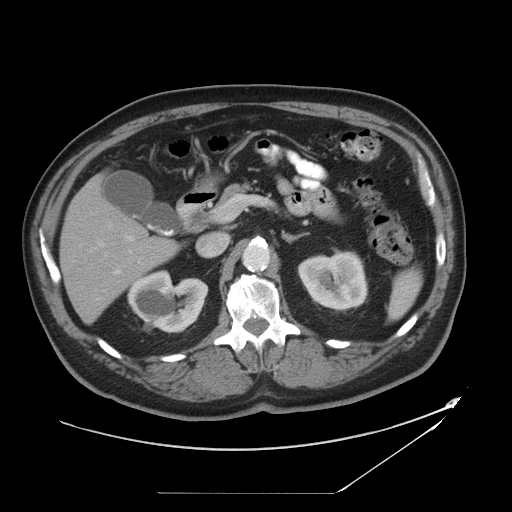
Contrast-enhanced abdominal CT, one axial slice. Slice 23 of 49 in the series (ordered by position). Soft-tissue window (W 400 / L 40 HU). 5 mm slice thickness. 512 × 512 image matrix. Male patient, age 72 years. From the clinical record (not read from this slice): diagnosis: colorectal cancer liver metastases, imaged before liver resection; multiple liver metastases: no; largest metastasis: 2.5 cm; disease in both lobes: no.
Structures marked on this image (manually delineated by an expert):
- hepatic veins: bounding box <97,223,112,247> (left, top, right, bottom; pixels)
- liver: <62,182,176,321>
- planned liver remnant (the part of the liver to remain after resection): <62,181,176,321>
- portal vein (with intrahepatic branches): <113,210,216,275>